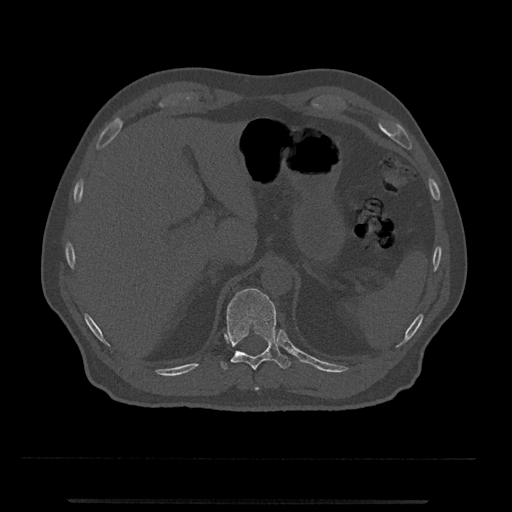
CT including the spine, one axial slice. Slice 465 of 797 in the series (ordered by position). Reconstruction kernel Br40s/3. Bone window (W 1800 / L 400 HU). 0.5 mm slice thickness. 512 × 512 image matrix, field of view 419 × 419 mm. Male patient, age 63 years. Case-level facts recorded for this patient, not image findings: primary cancer: prostate.
Annotated regions visible in this slice (semi-automatically segmented with operator editing):
- T10 vertebra: bounding box [x1, y1, x2, y2] px = [255, 387, 259, 390]
- T11 vertebra: [220, 288, 291, 370]